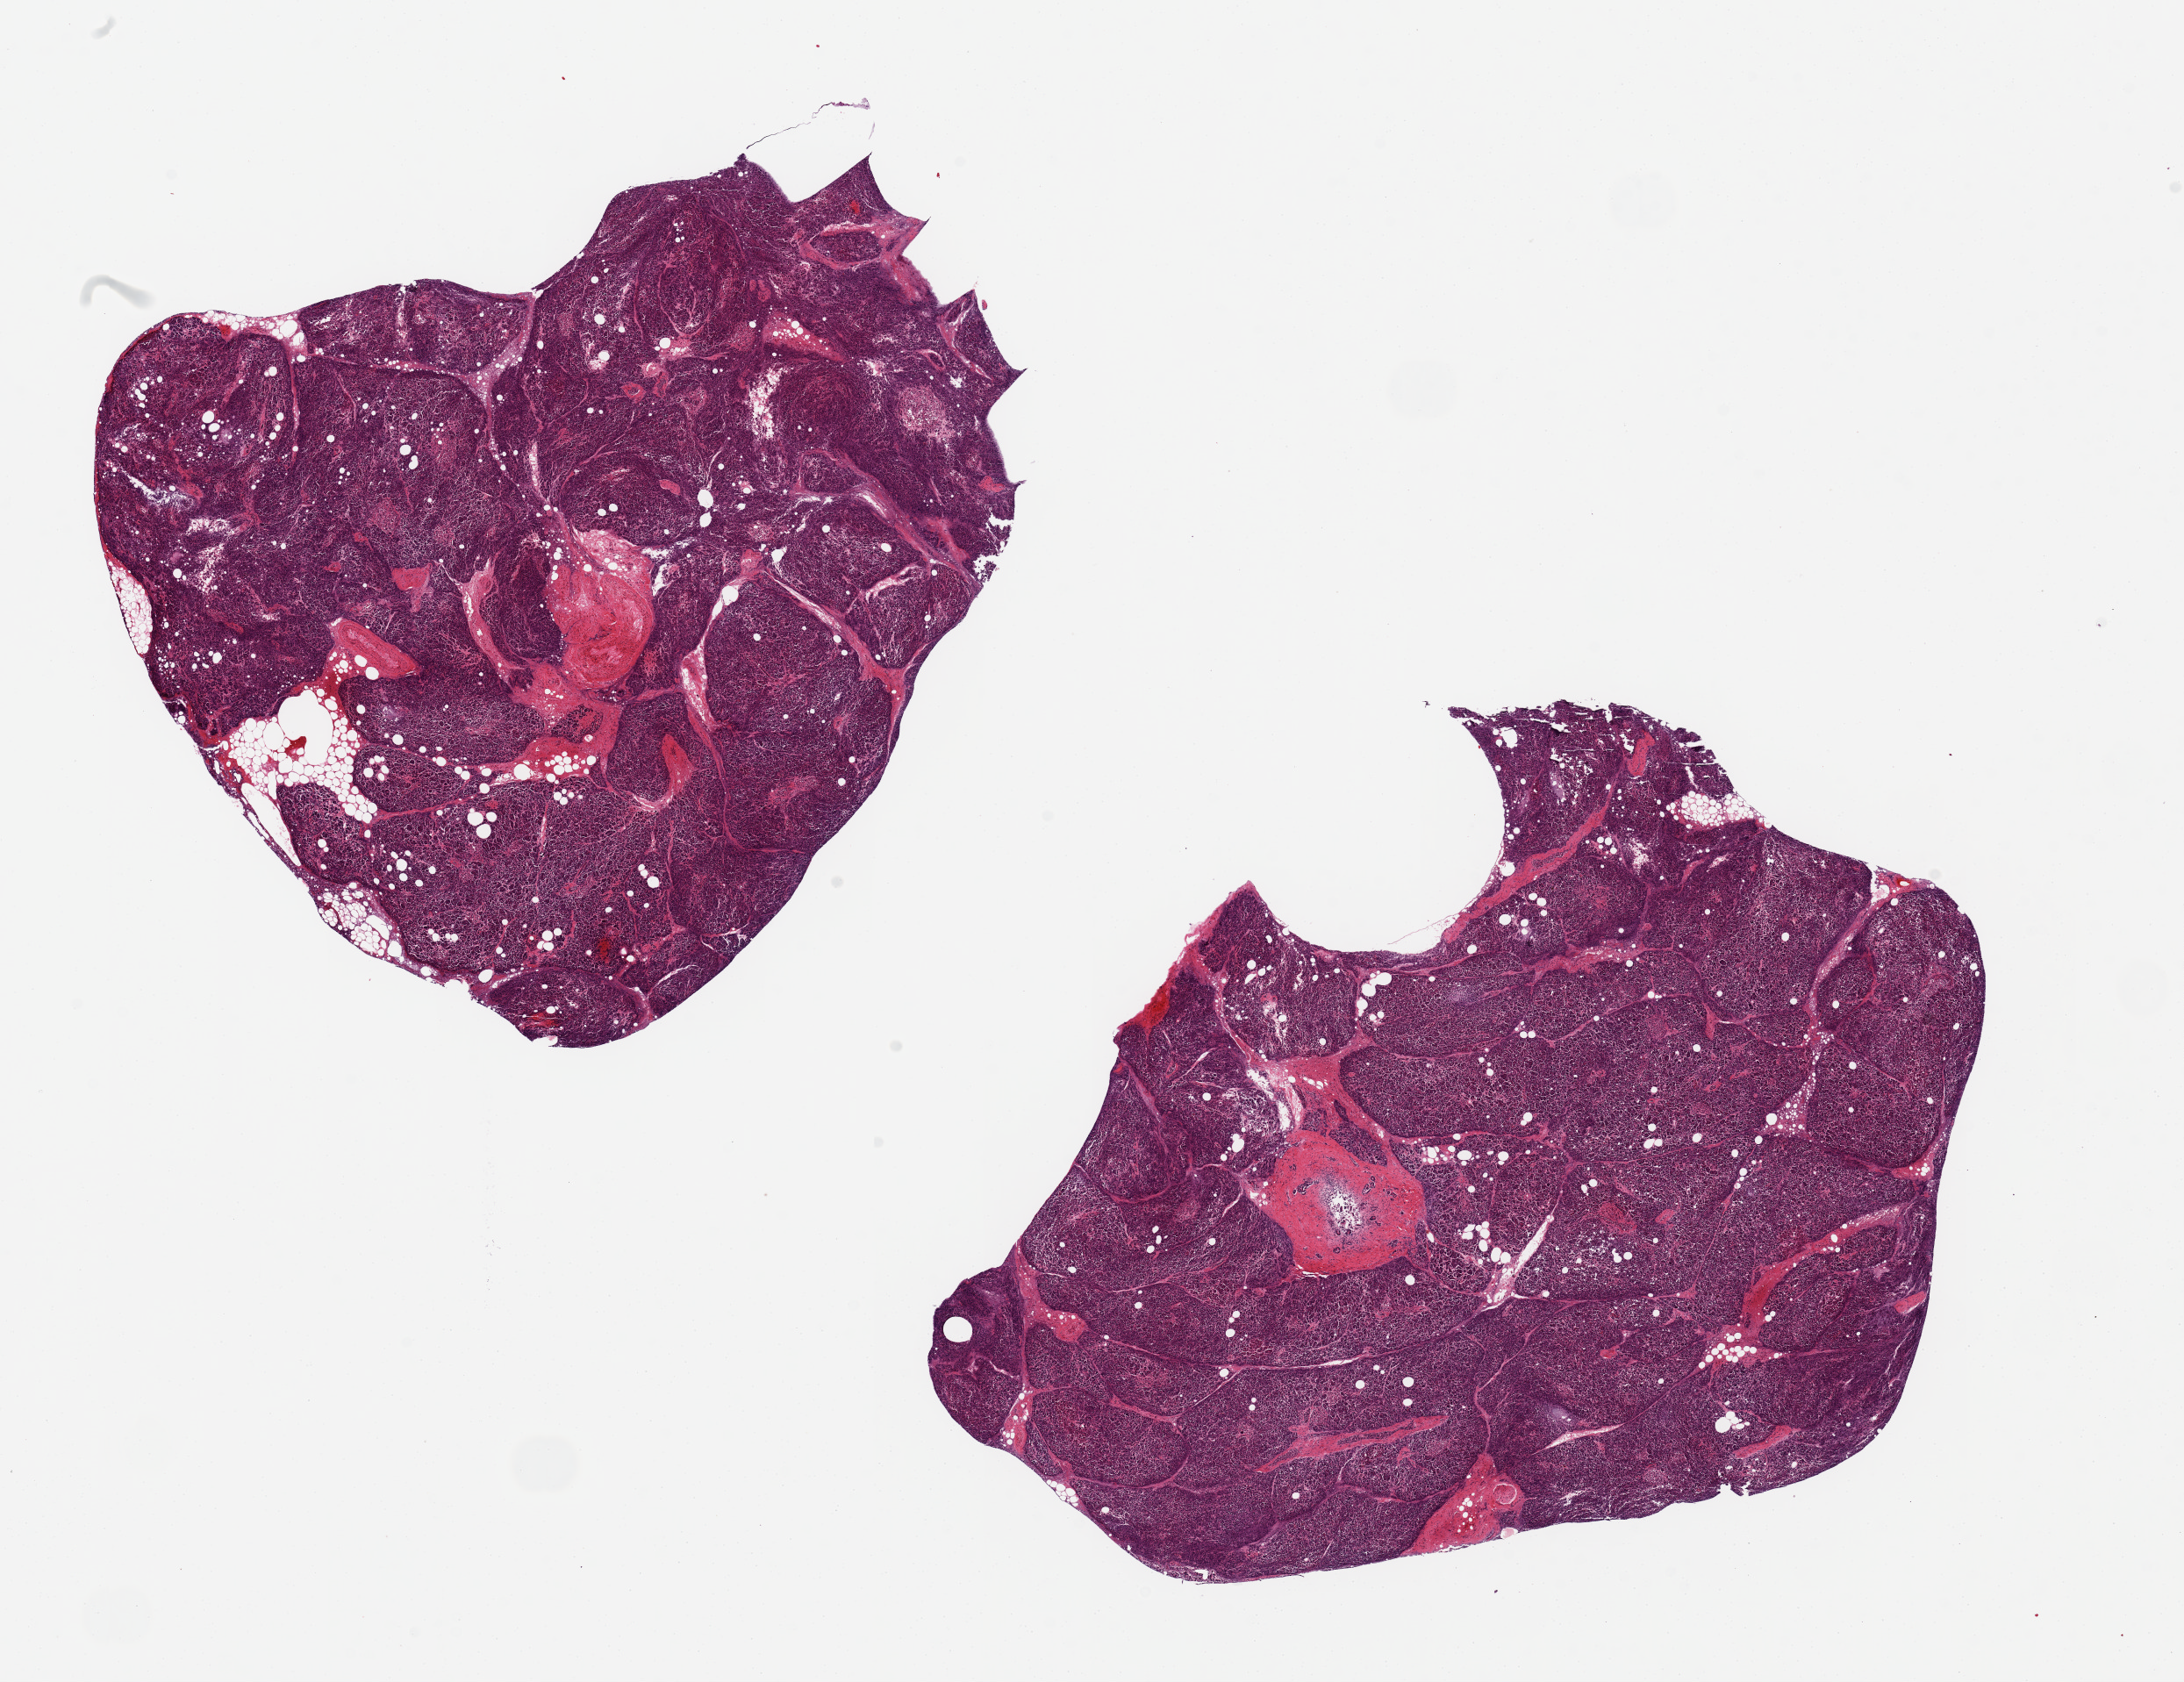
Digitized hematoxylin and eosin (H&E)-stained section, brightfield, a low-resolution overview of the entire scanned area, about 19.7 x 15.2 mm (from a 20x scan), PAXgene-fixed, paraffin-embedded tissue, sampled site (target tissue): pancreas, tissue donor sample.
Pathologist's review note for this sample: 2 pieces, 9x7 & 8x8 mm; ~5% intra-parenchymal fat.